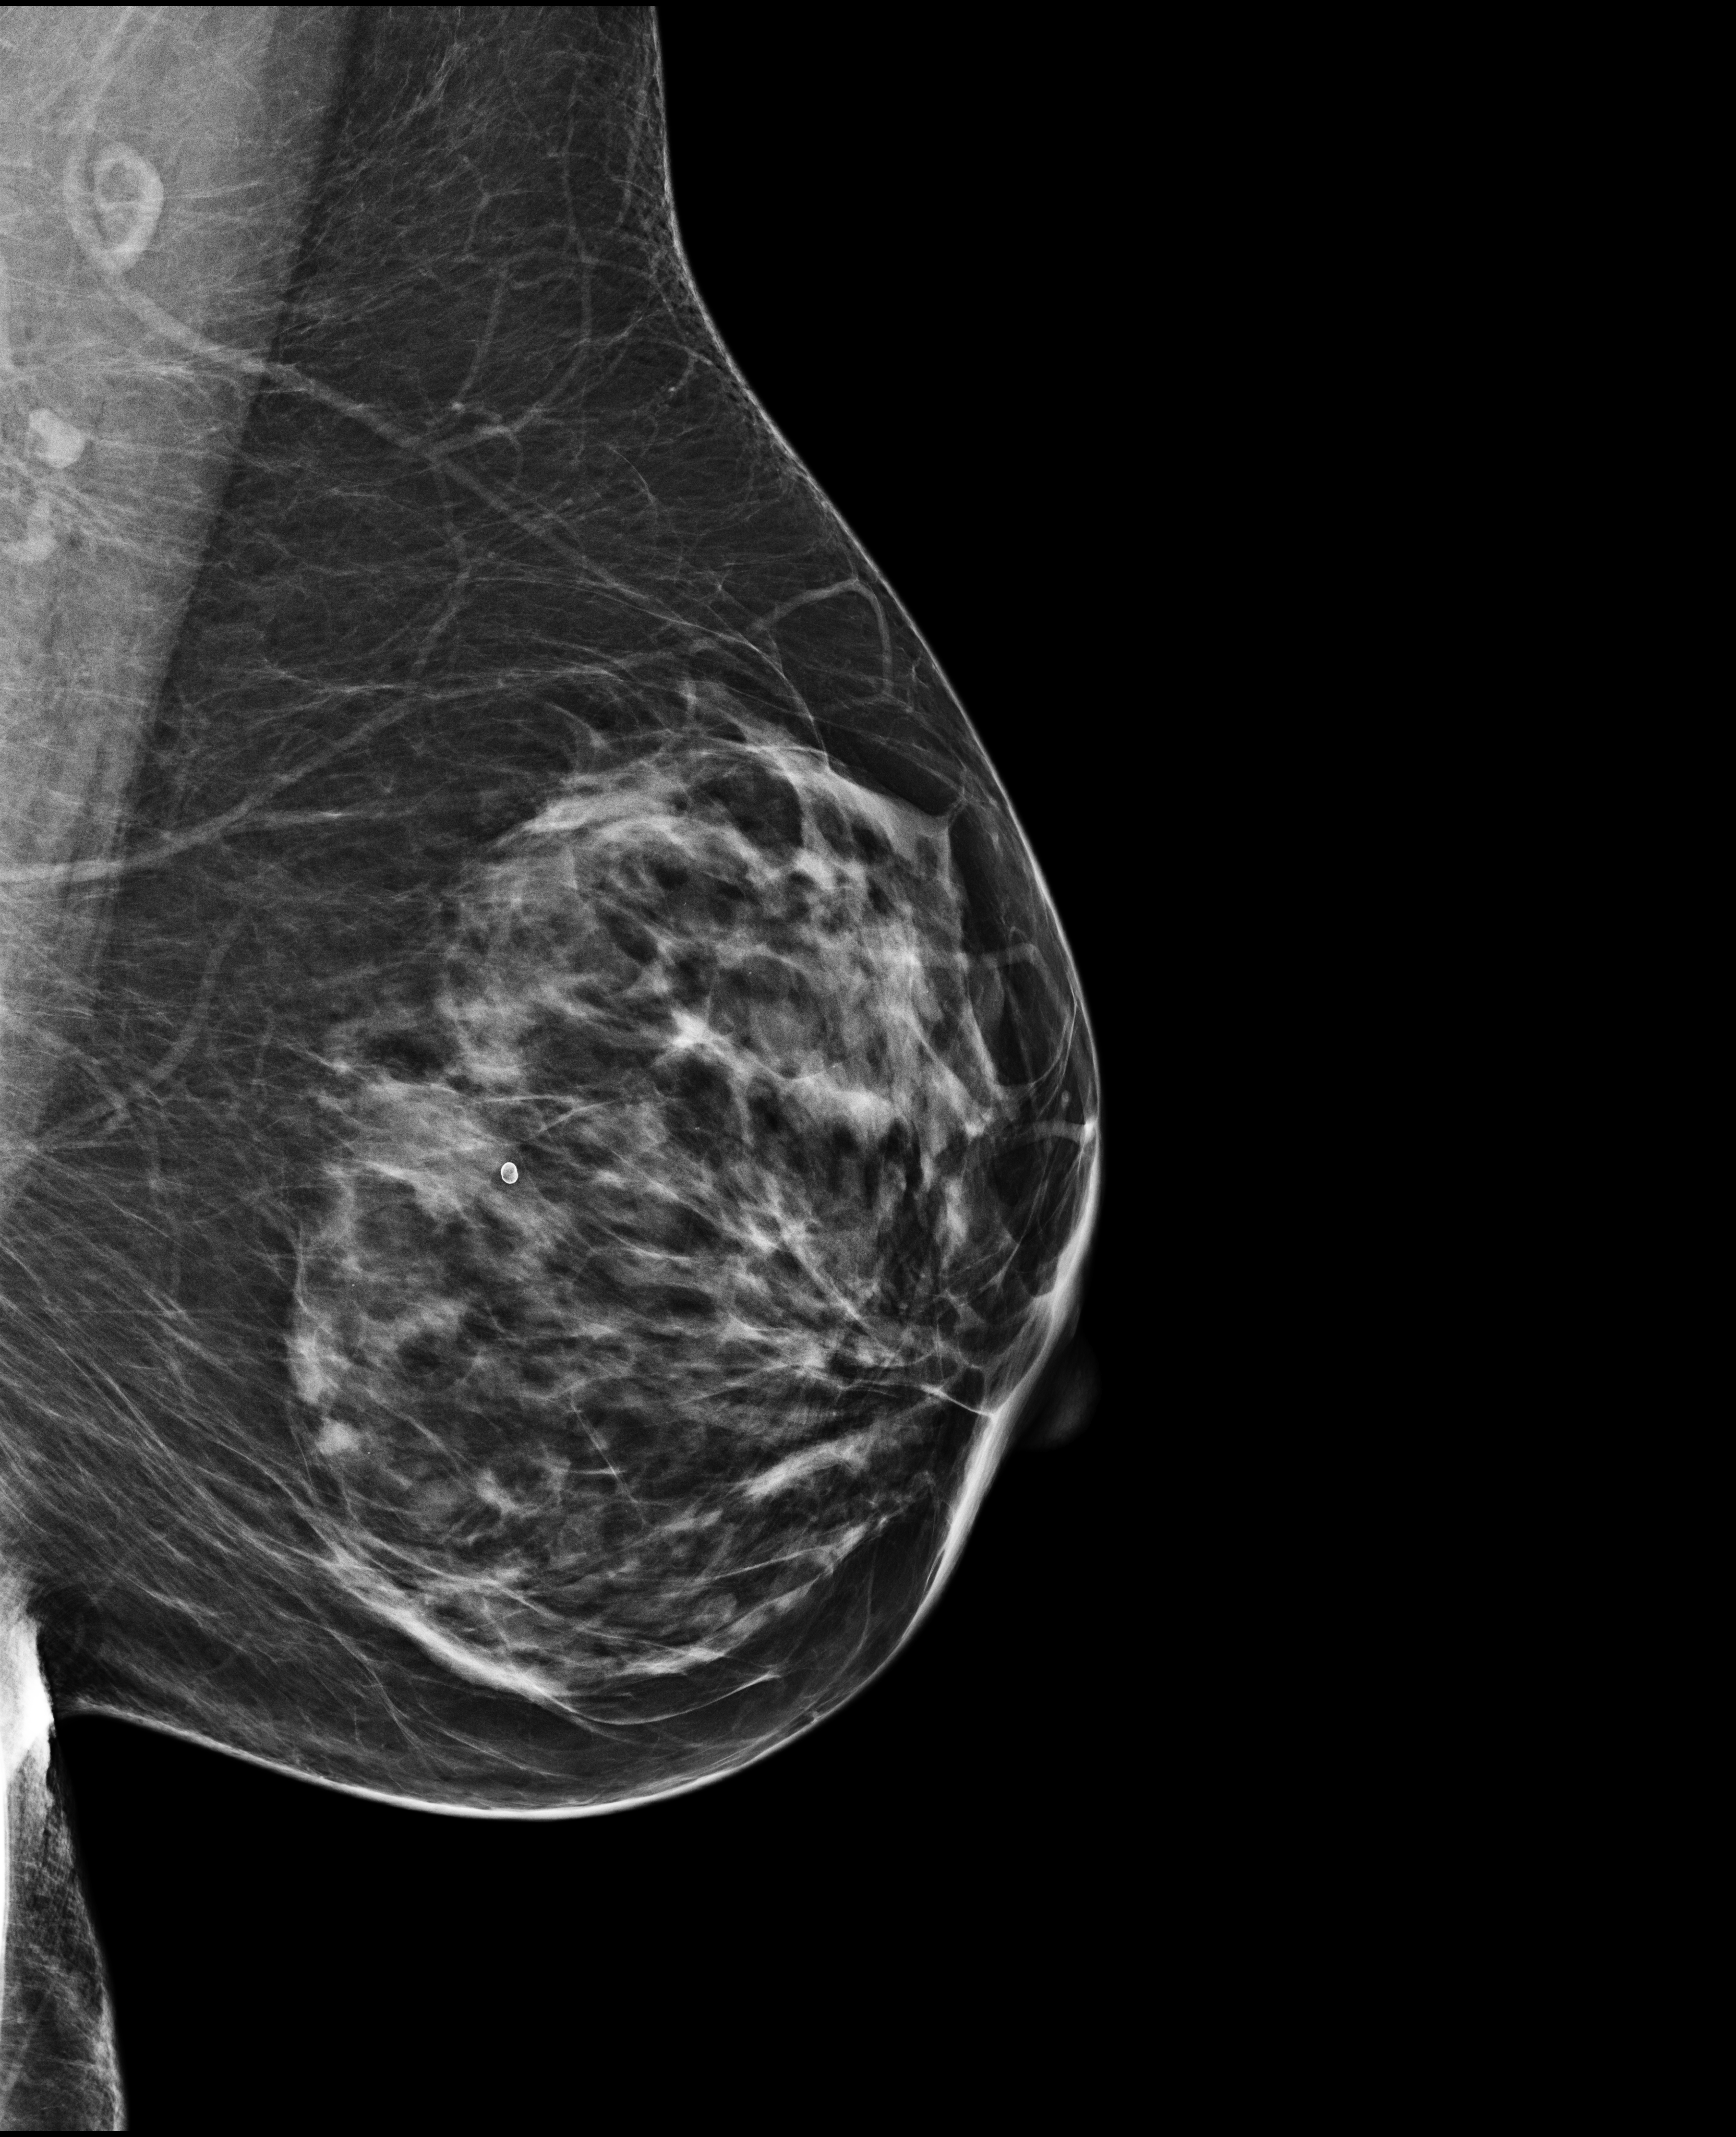
Screening examination, compressed breast thickness 79 mm. Patient aged 58 years (female).
Image type: full-field digital mammogram. Breast: left. Projection: medio-lateral oblique projection.